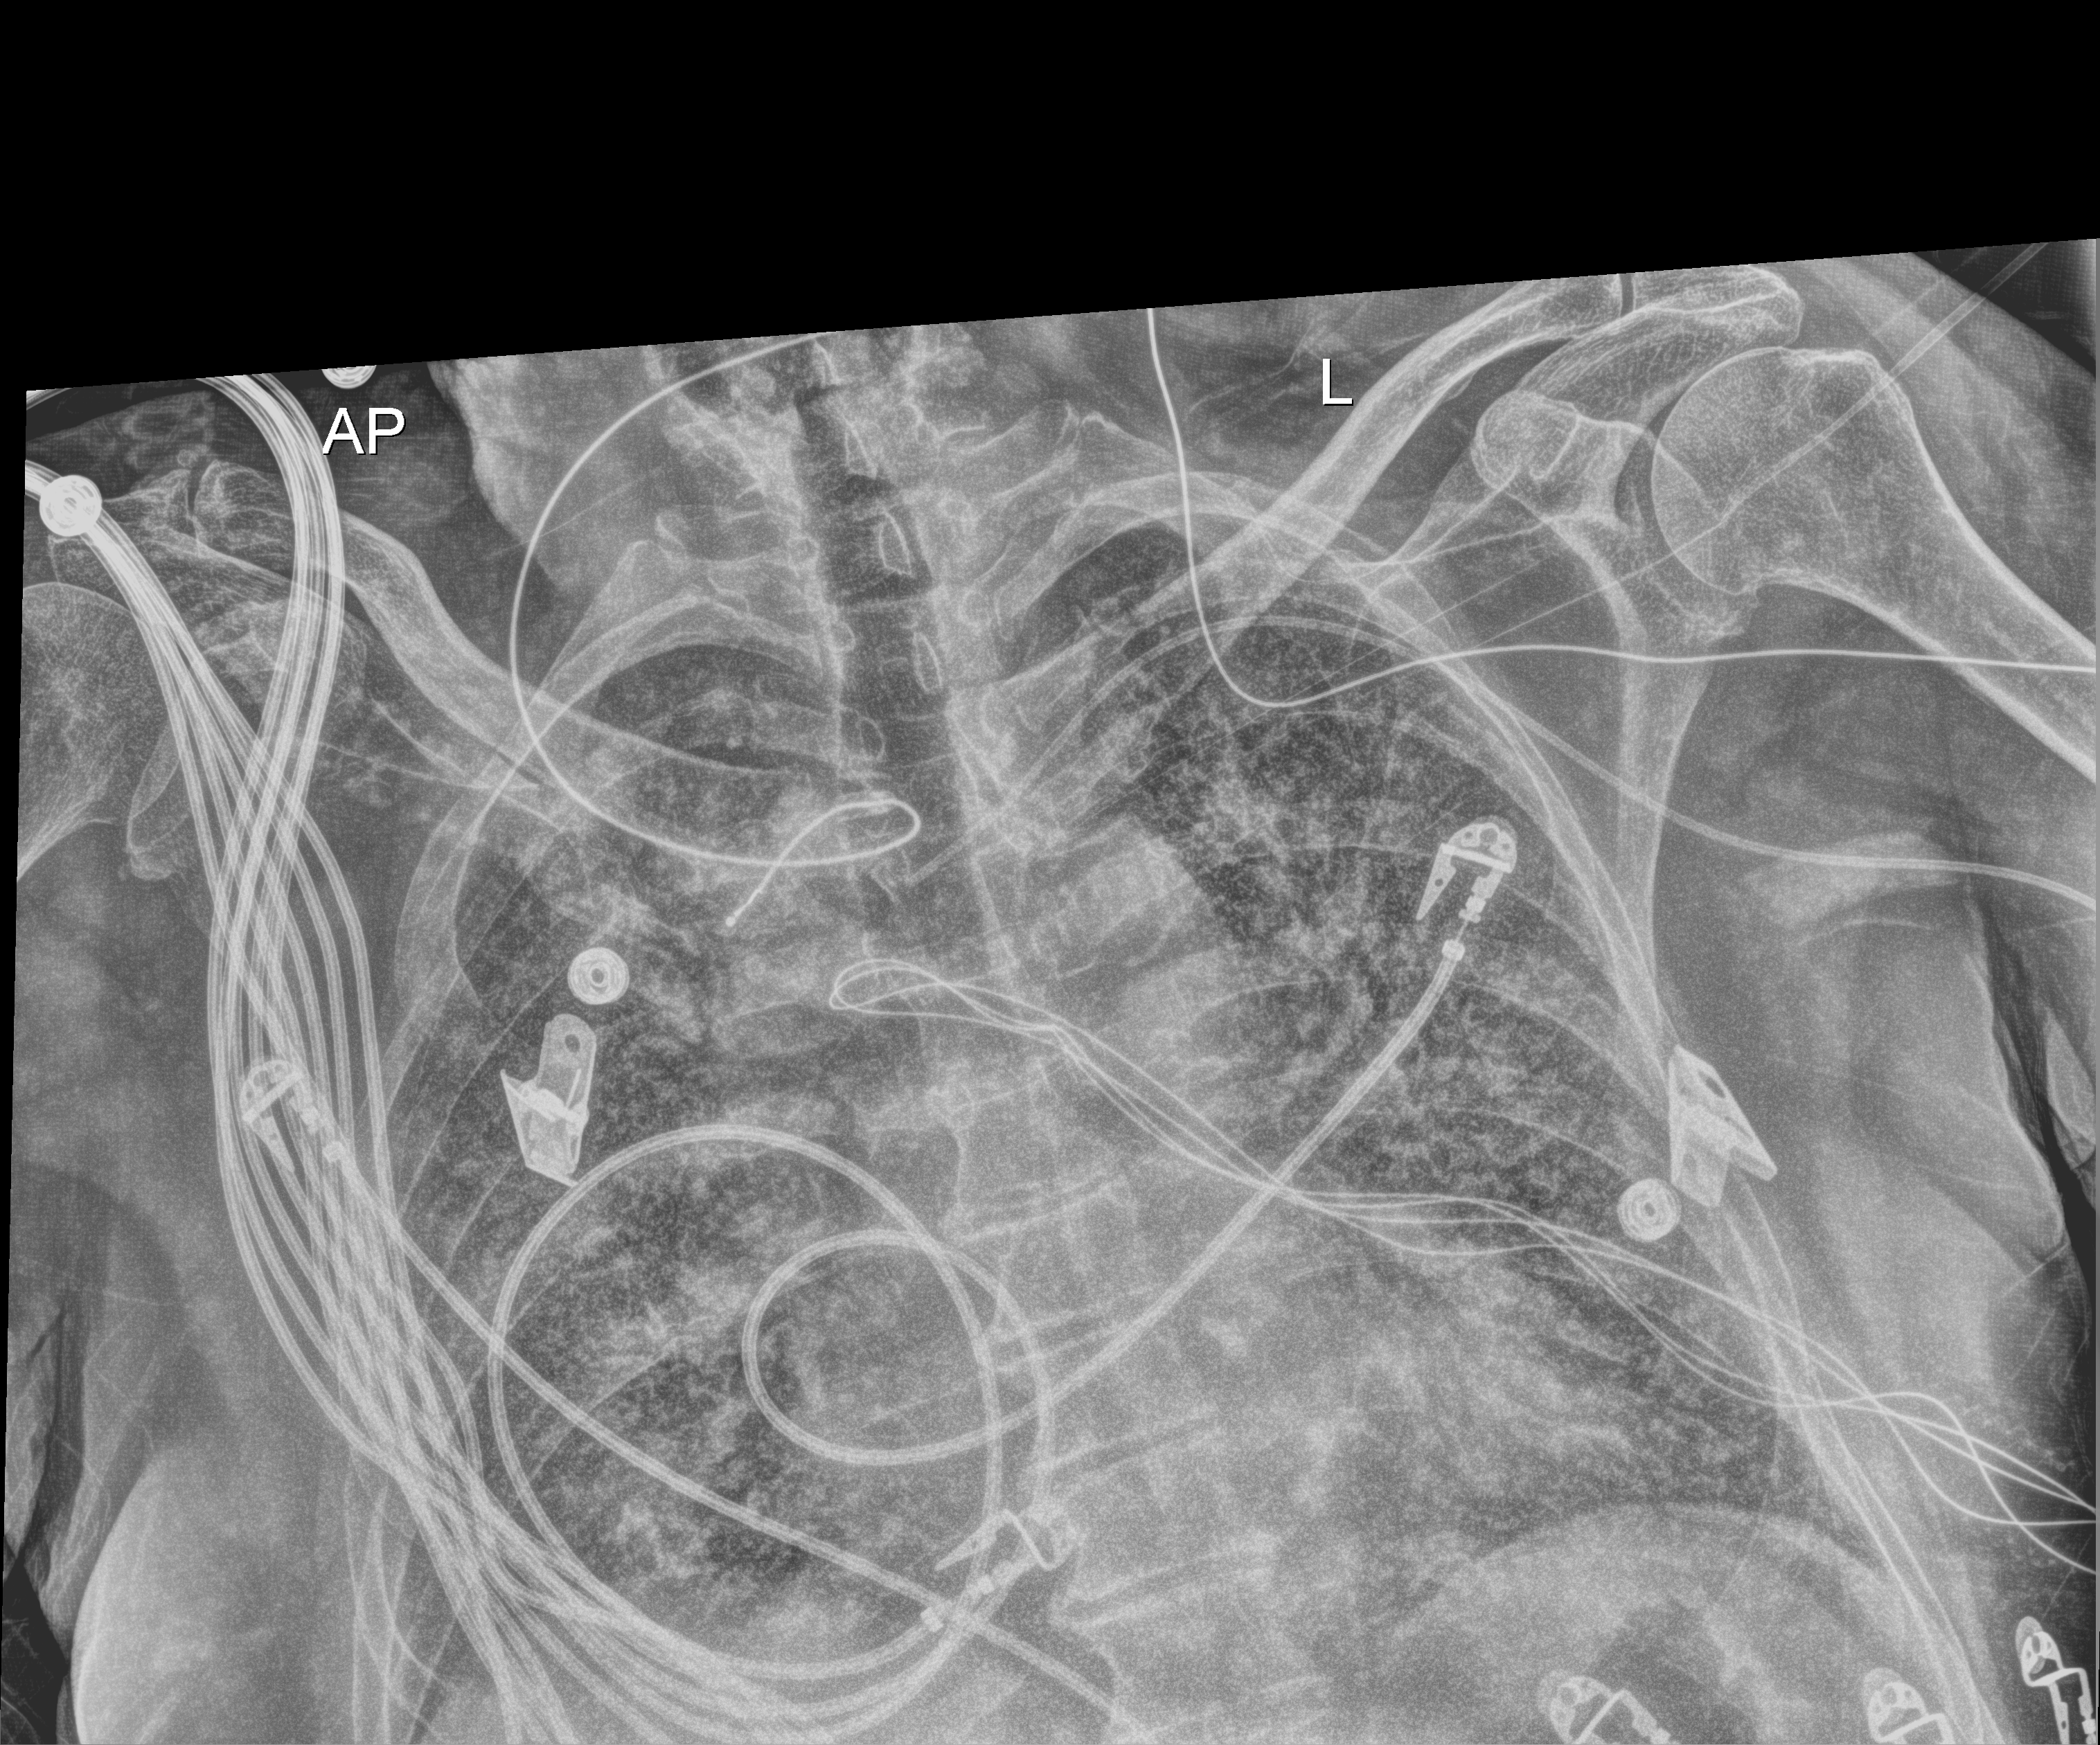
Portable chest radiograph, anteroposterior (AP) projection. Male patient hospitalised with COVID-19, age 75–90 years.
Admission-level facts for this patient (not findings on this image; timing relative to this image not recorded): other chronic lung disease (admission record): no; mechanically ventilated during this hospital stay: yes.